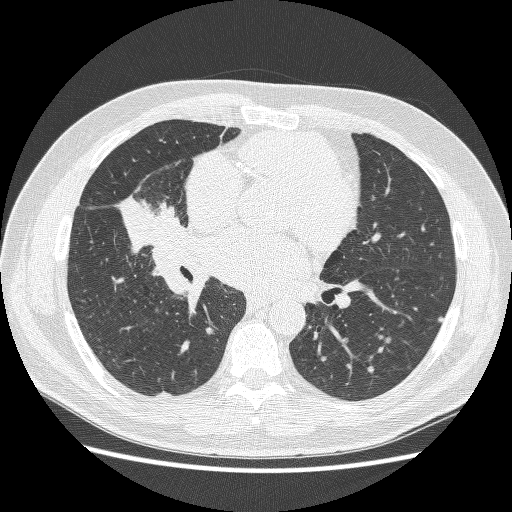
Chest CT (low-dose screening protocol), one axial image. Baseline screening round. Lung window (W 1500 / L -600 HU). 1.25 mm slice thickness. Slice 133 of 251 in the series. 512 × 512 image matrix, field of view 360 × 360 mm. Male, age 59 years at enrolment. Former smoker at enrolment.
Expert-annotated lung lesion, bounding box [x1, y1, x2, y2] px = [117, 178, 196, 256]. Screening reader's record for this exam: no non-calcified nodule ≥4 mm recorded. Lung cancer was diagnosed 24 days after this screen: adenocarcinoma, NOS, right middle lobe, poorly differentiated (G3), stage IV (AJCC 6th edition), 54 mm at pathology.